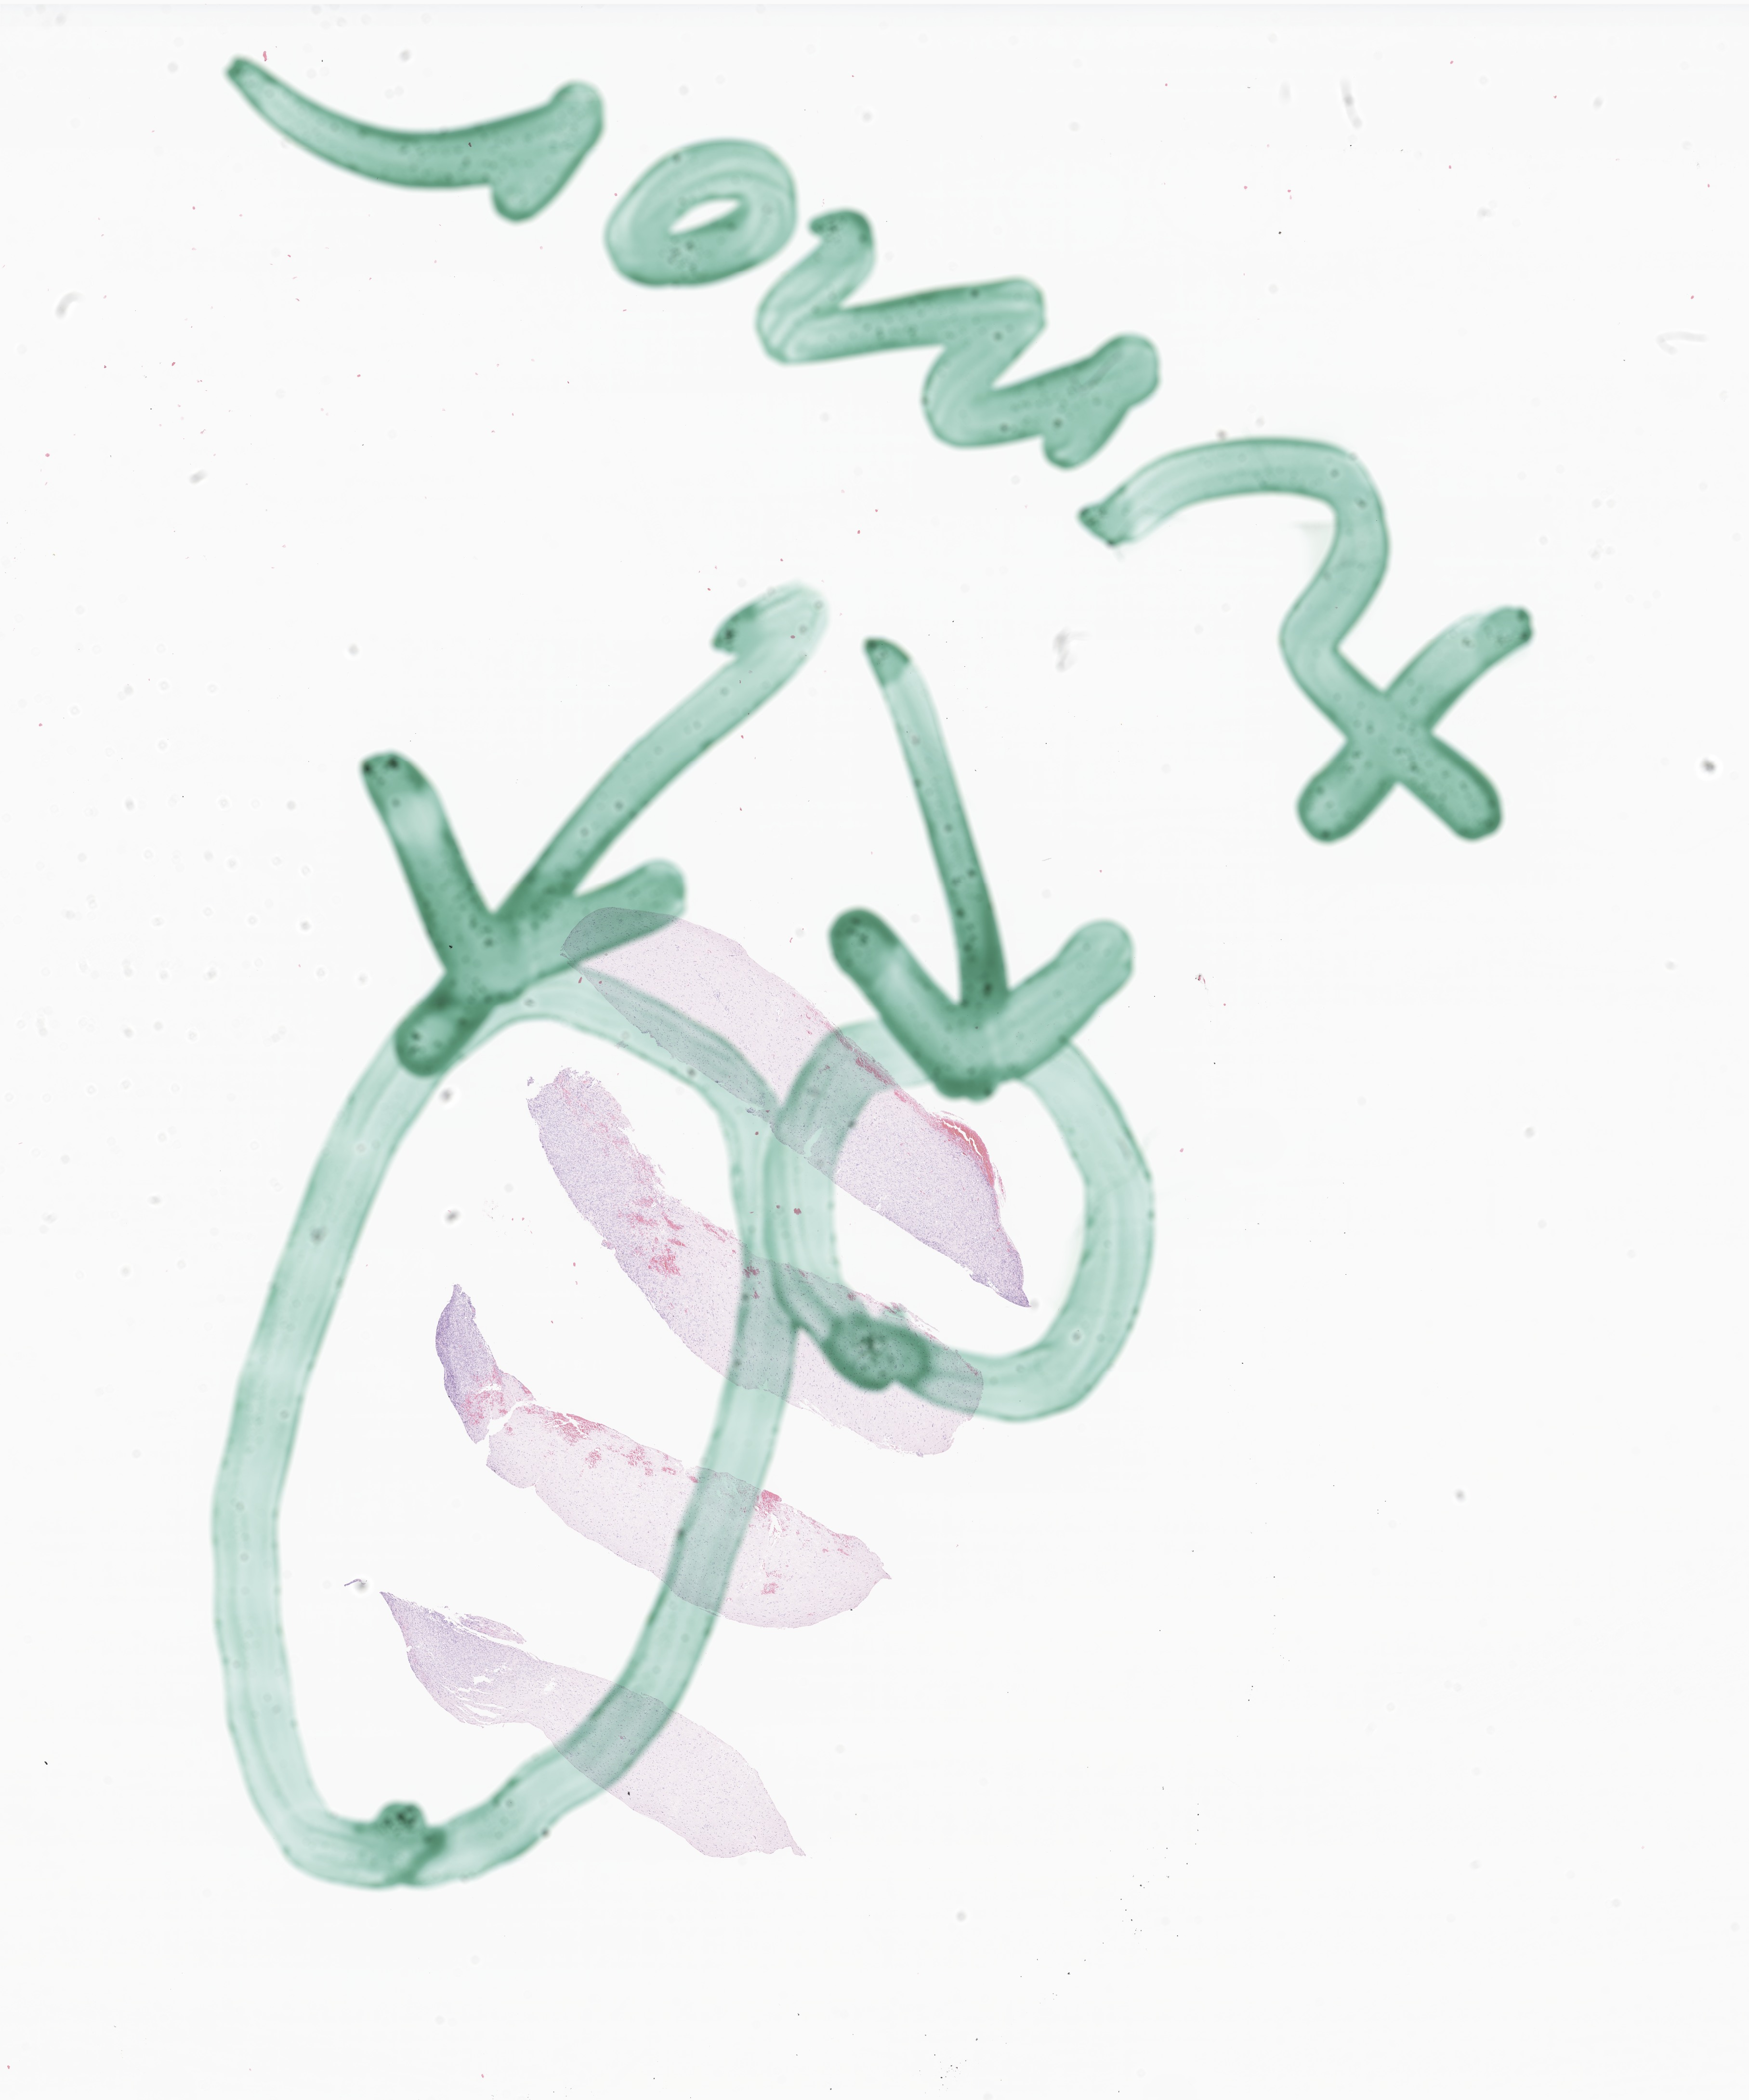
Whole-slide image, hematoxylin and eosin (H&E) stain of tumor tissue from the brain, low-resolution overview of the scanned area, about 15.3 x 18.4 mm, formalin-fixed paraffin-embedded section. Patient: female, age 361 days.
Diagnosis: Atypical teratoid/rhabdoid tumor.